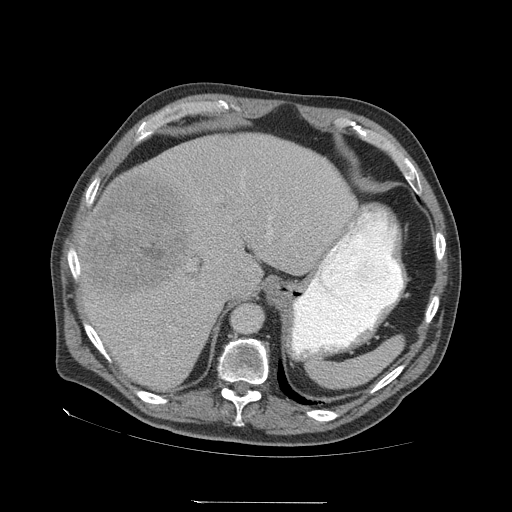
Contrast-enhanced abdominal CT (liver protocol), one axial slice; soft-tissue window (W 400 / L 40 HU); 2.5 mm slice thickness; 512 × 512 image matrix, field of view 460 × 460 mm. Case-level facts recorded for this patient, not image findings: diagnosis: hepatocellular carcinoma (patient treated with transarterial chemoembolisation; whether this scan precedes or follows treatment is not stated here); TNM stage (as recorded): Stage-I; Child-Pugh class: A; tumour differentiation: well differentiated.
Annotated regions visible in this slice (semi-automatically segmented with operator editing):
- liver parenchyma outside the tumour (the mass and vessels are separate outlines, so this box may not span the whole liver): bounding box (x1, y1, x2, y2) in pixels: (78, 132, 356, 390)
- mass: (83, 174, 193, 302)
- liver vessels: (99, 217, 273, 349)